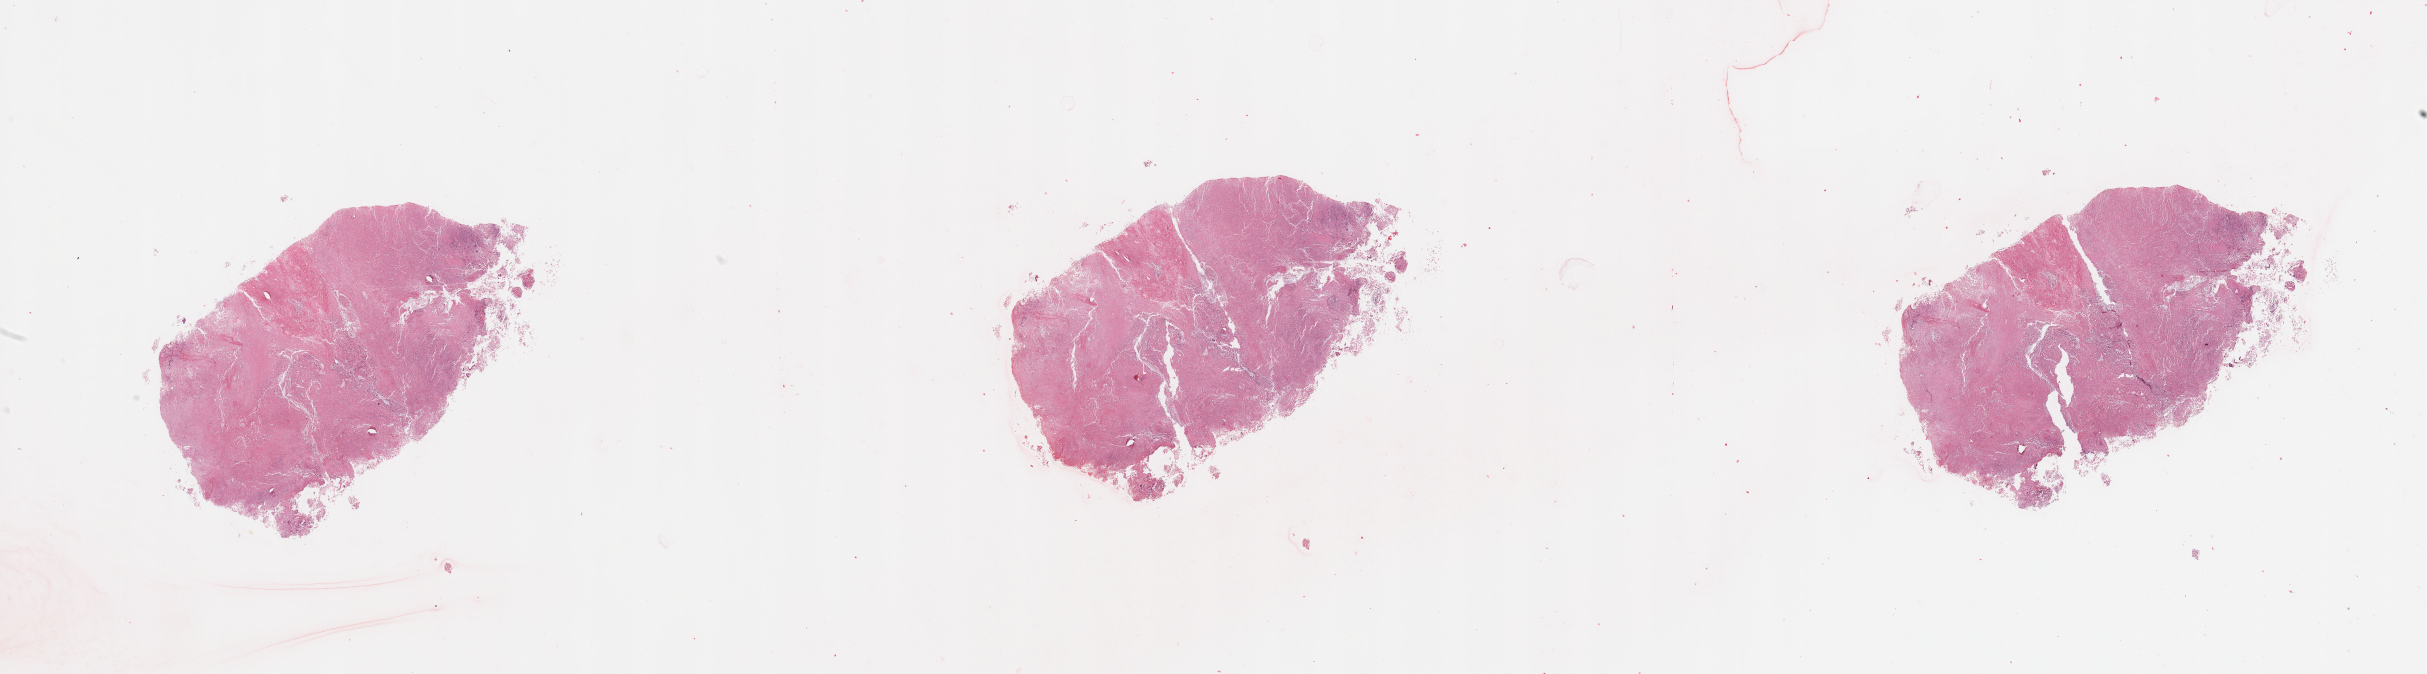
Whole-slide histology image, H&E — a low-resolution overview of the entire scanned area, about 38.4 x 10.7 mm (acquisition: 20x scan), pancreas, tumour tissue. Male, 72 y/o. Histologic grade: G2 (moderately differentiated).
AJCC pathologic stage: IB. Diagnosis: Infiltrating duct carcinoma, NOS.